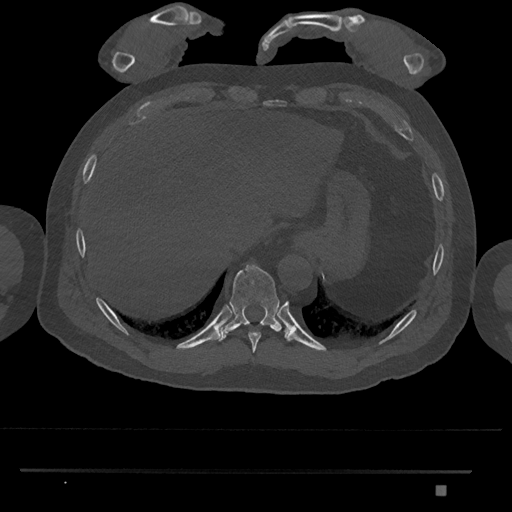
CT including the spine, one axial slice. Position 1020 of 1134 along the scan axis. 120 kVp. Bone window (W 1800 / L 400 HU). 0.5 mm slice thickness. 512 × 512 image matrix, field of view 429 × 429 mm. Male patient, age 65 years. Case-level facts recorded for this patient, not image findings: primary cancer: prostate.
Structures marked on this image (semi-automatically segmented with operator editing):
- T10 vertebra: bounding box <218,264,285,342> (left, top, right, bottom; pixels)
- T9 vertebra: <248,324,262,353>